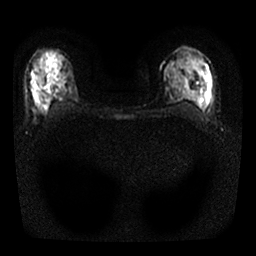
Breast MRI, one axial slice; position 14 of 25 along the scan axis; diffusion-weighted series; image 2 of 4 stored at this slice position (different b-values; order by instance number); 1.5 T; 4 mm slice thickness; 256 × 256 image matrix, field of view 300 × 300 mm. Female patient.
Outlined on this slice (manually delineated by an expert):
- tumour on diffusion-weighted imaging: box from (x=34, y=63) to (x=60, y=104) px